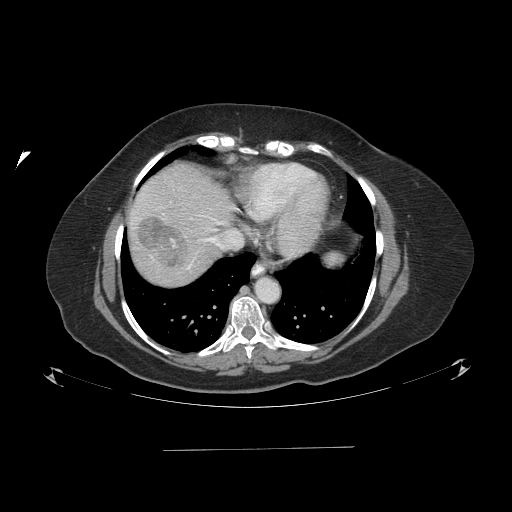
Contrast-enhanced abdominal CT (liver protocol), one axial slice. Position 79 of 103 along the scan axis. One of 2 acquisitions stored at this slice position. Soft-tissue window (W 400 / L 40 HU). 2.5 mm slice thickness. 512 × 512 image matrix, field of view 500 × 500 mm. Case-level facts recorded for this patient, not image findings: diagnosis: hepatocellular carcinoma (patient treated with transarterial chemoembolisation; whether this scan precedes or follows treatment is not stated here); TNM stage (as recorded): Stage-IIIA; Child-Pugh class: A; tumour nodularity: multinodular; tumour size: 5.2 cm.
Outlined on this slice (semi-automatically segmented with operator editing):
- liver parenchyma outside the tumour (the mass and vessels are separate outlines, so this box may not span the whole liver): bounding box <128,162,234,286> (left, top, right, bottom; pixels)
- mass: <137,216,187,269>
- liver vessels: <135,215,222,269>